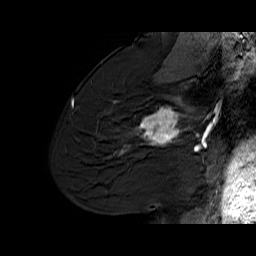
Breast MRI (dynamic contrast-enhanced), one sagittal slice. Dynamic contrast-enhanced series, time point 2 of 6 at this slice position (early post-contrast). 1.5 T. TE 6.1 ms, TR 32.9 ms. 4 mm slice thickness. 256 × 256 image matrix, field of view 220 × 220 mm. Female patient. From the clinical record (not read from this slice): setting: breast cancer imaged before/during neoadjuvant chemotherapy; receptor status: HER2-positive.
Annotated regions visible in this slice (semi-automatic segmentation, software-assisted and operator-edited):
- analysis volume of interest (the breast-tissue region the enhancement analysis was run in; not a lesion): bounding box <127,95,194,165> (left, top, right, bottom; pixels)
- tumour enhancement mask (voxels above the 100 % enhancement threshold inside the analysis volume of interest): <135,96,186,145>